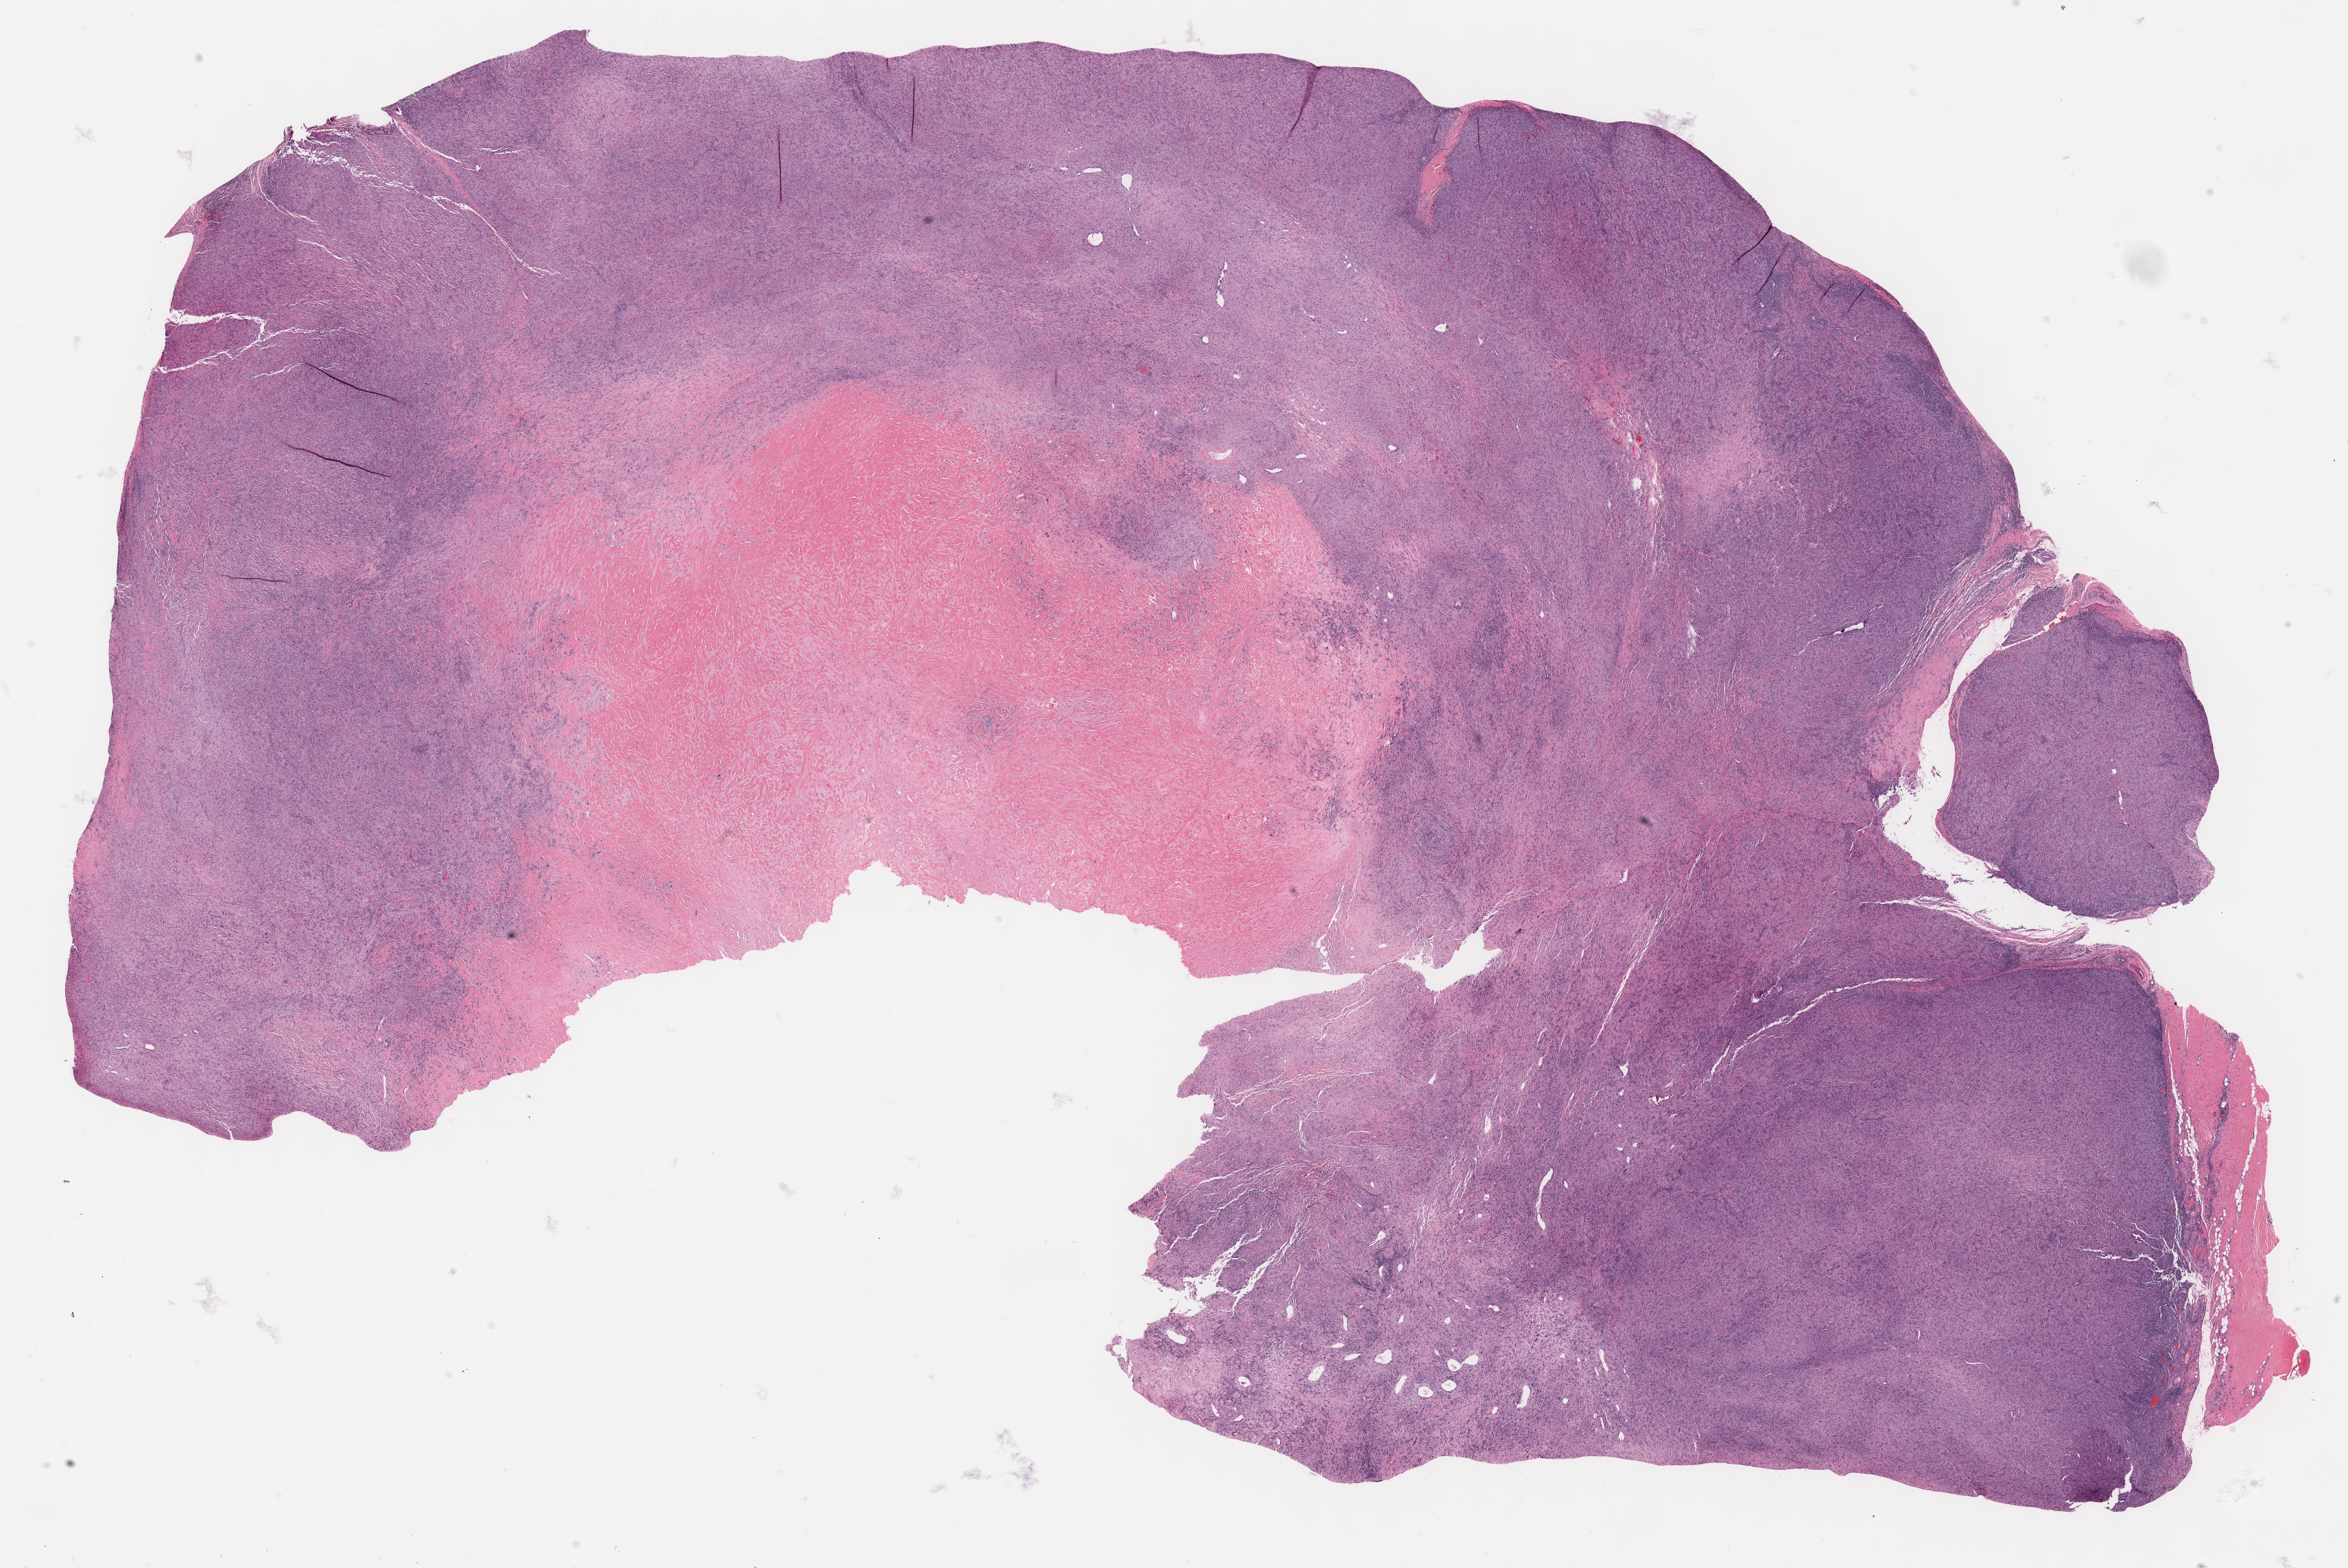
H&E-stained whole-slide image, a low-resolution overview of the entire scanned area, about 27.7 x 18.5 mm (slide scanned at 40x). Formalin-fixed paraffin-embedded (FFPE) diagnostic section. Connective, subcutaneous and other soft tissues, primary tumour sample. Female patient.
• histologic diagnosis: Malignant fibrous histiocytoma (connective, subcutaneous and other soft tissues of trunk, NOS)